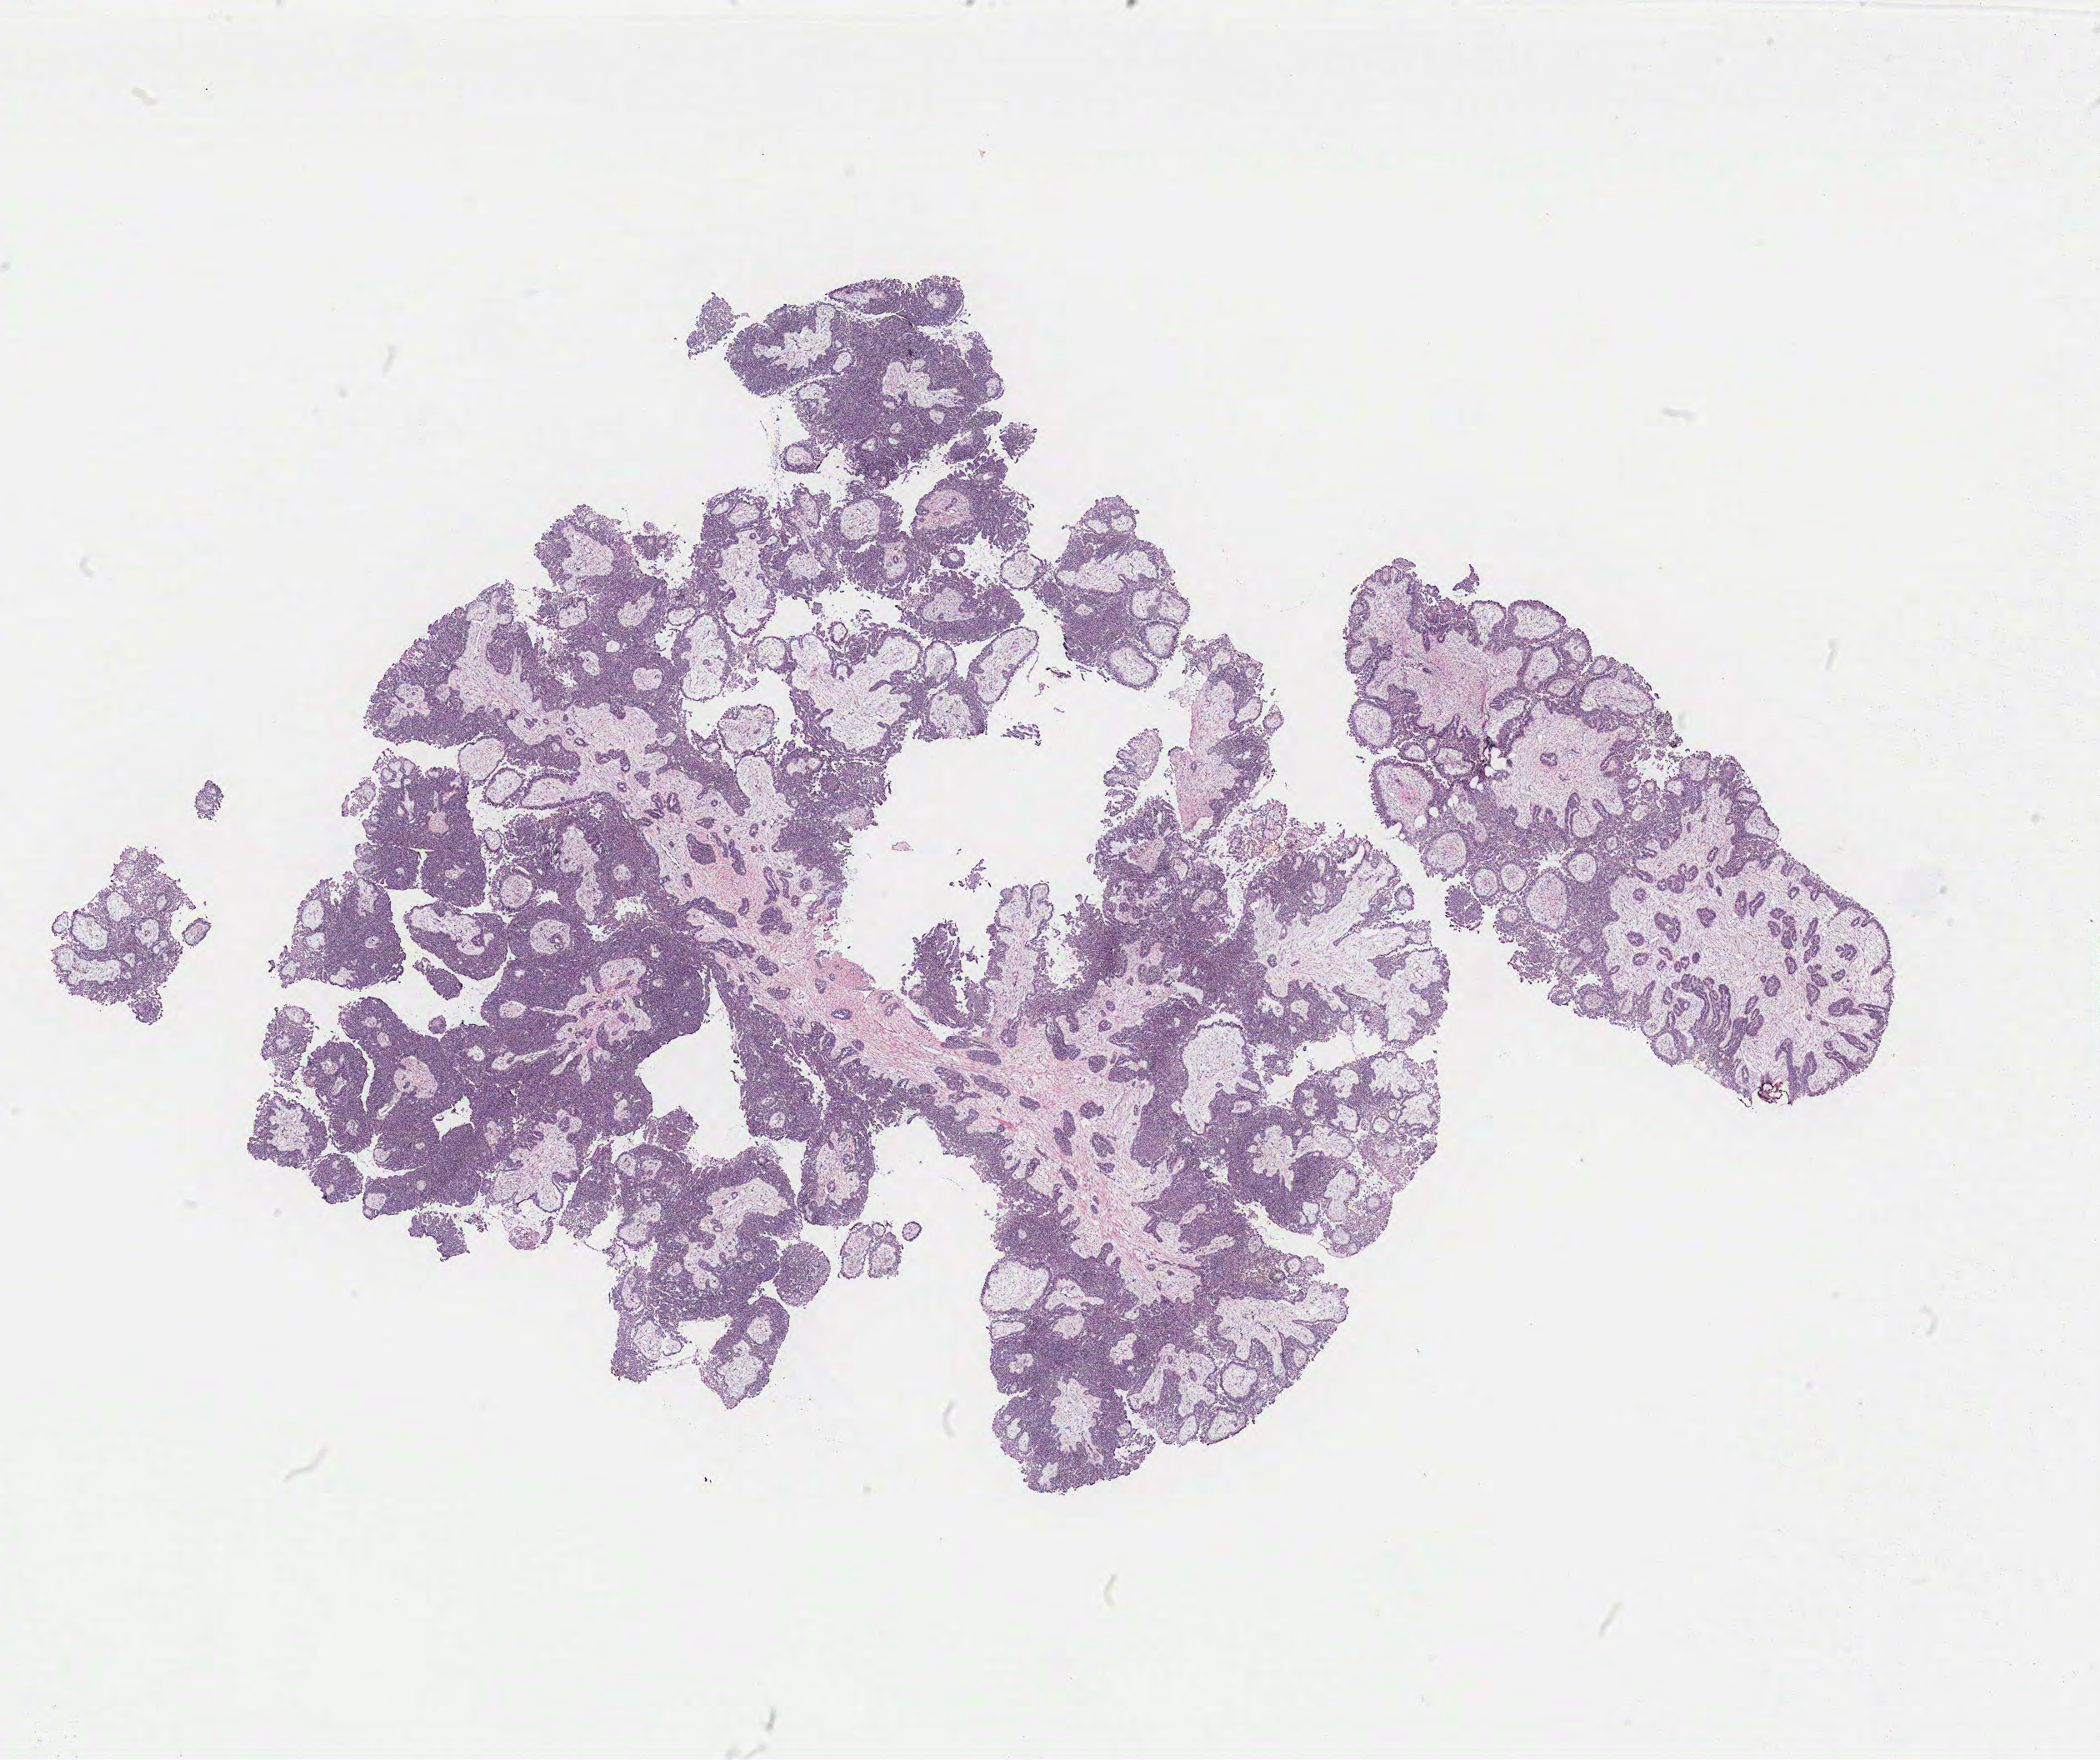
Whole-slide histology image, H&E, shown as a low-resolution overview of the whole scanned area (about 20.2 x 16.9 mm); tumour tissue sample, ovary. 85-year-old female patient.
Primary tumour site (as recorded): fallopian tube. Diagnosis: Serous adenocarcinoma, NOS (fallopian tube).